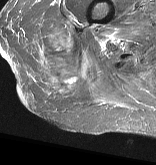
MRI of an extremity soft-tissue mass, one axial slice; slice 14 of 57 in the series (ordered by position); STIR; MR volume resampled by the dataset authors to the PET/CT grid (not the native acquisition matrix); 3.27 mm slice thickness; 156 × 165 image matrix, field of view 152 × 161 mm. Female patient. From the clinical record (not read from this slice): histological type: epithelioid sarcoma with vascular differentiation; site of the primary tumour: right buttock.
Annotated regions visible in this slice (expert contour drawn on MRI and transferred to this co-registered scan by the dataset authors):
- gross tumour volume (mass): bounding box <37,25,91,99> (left, top, right, bottom; pixels)